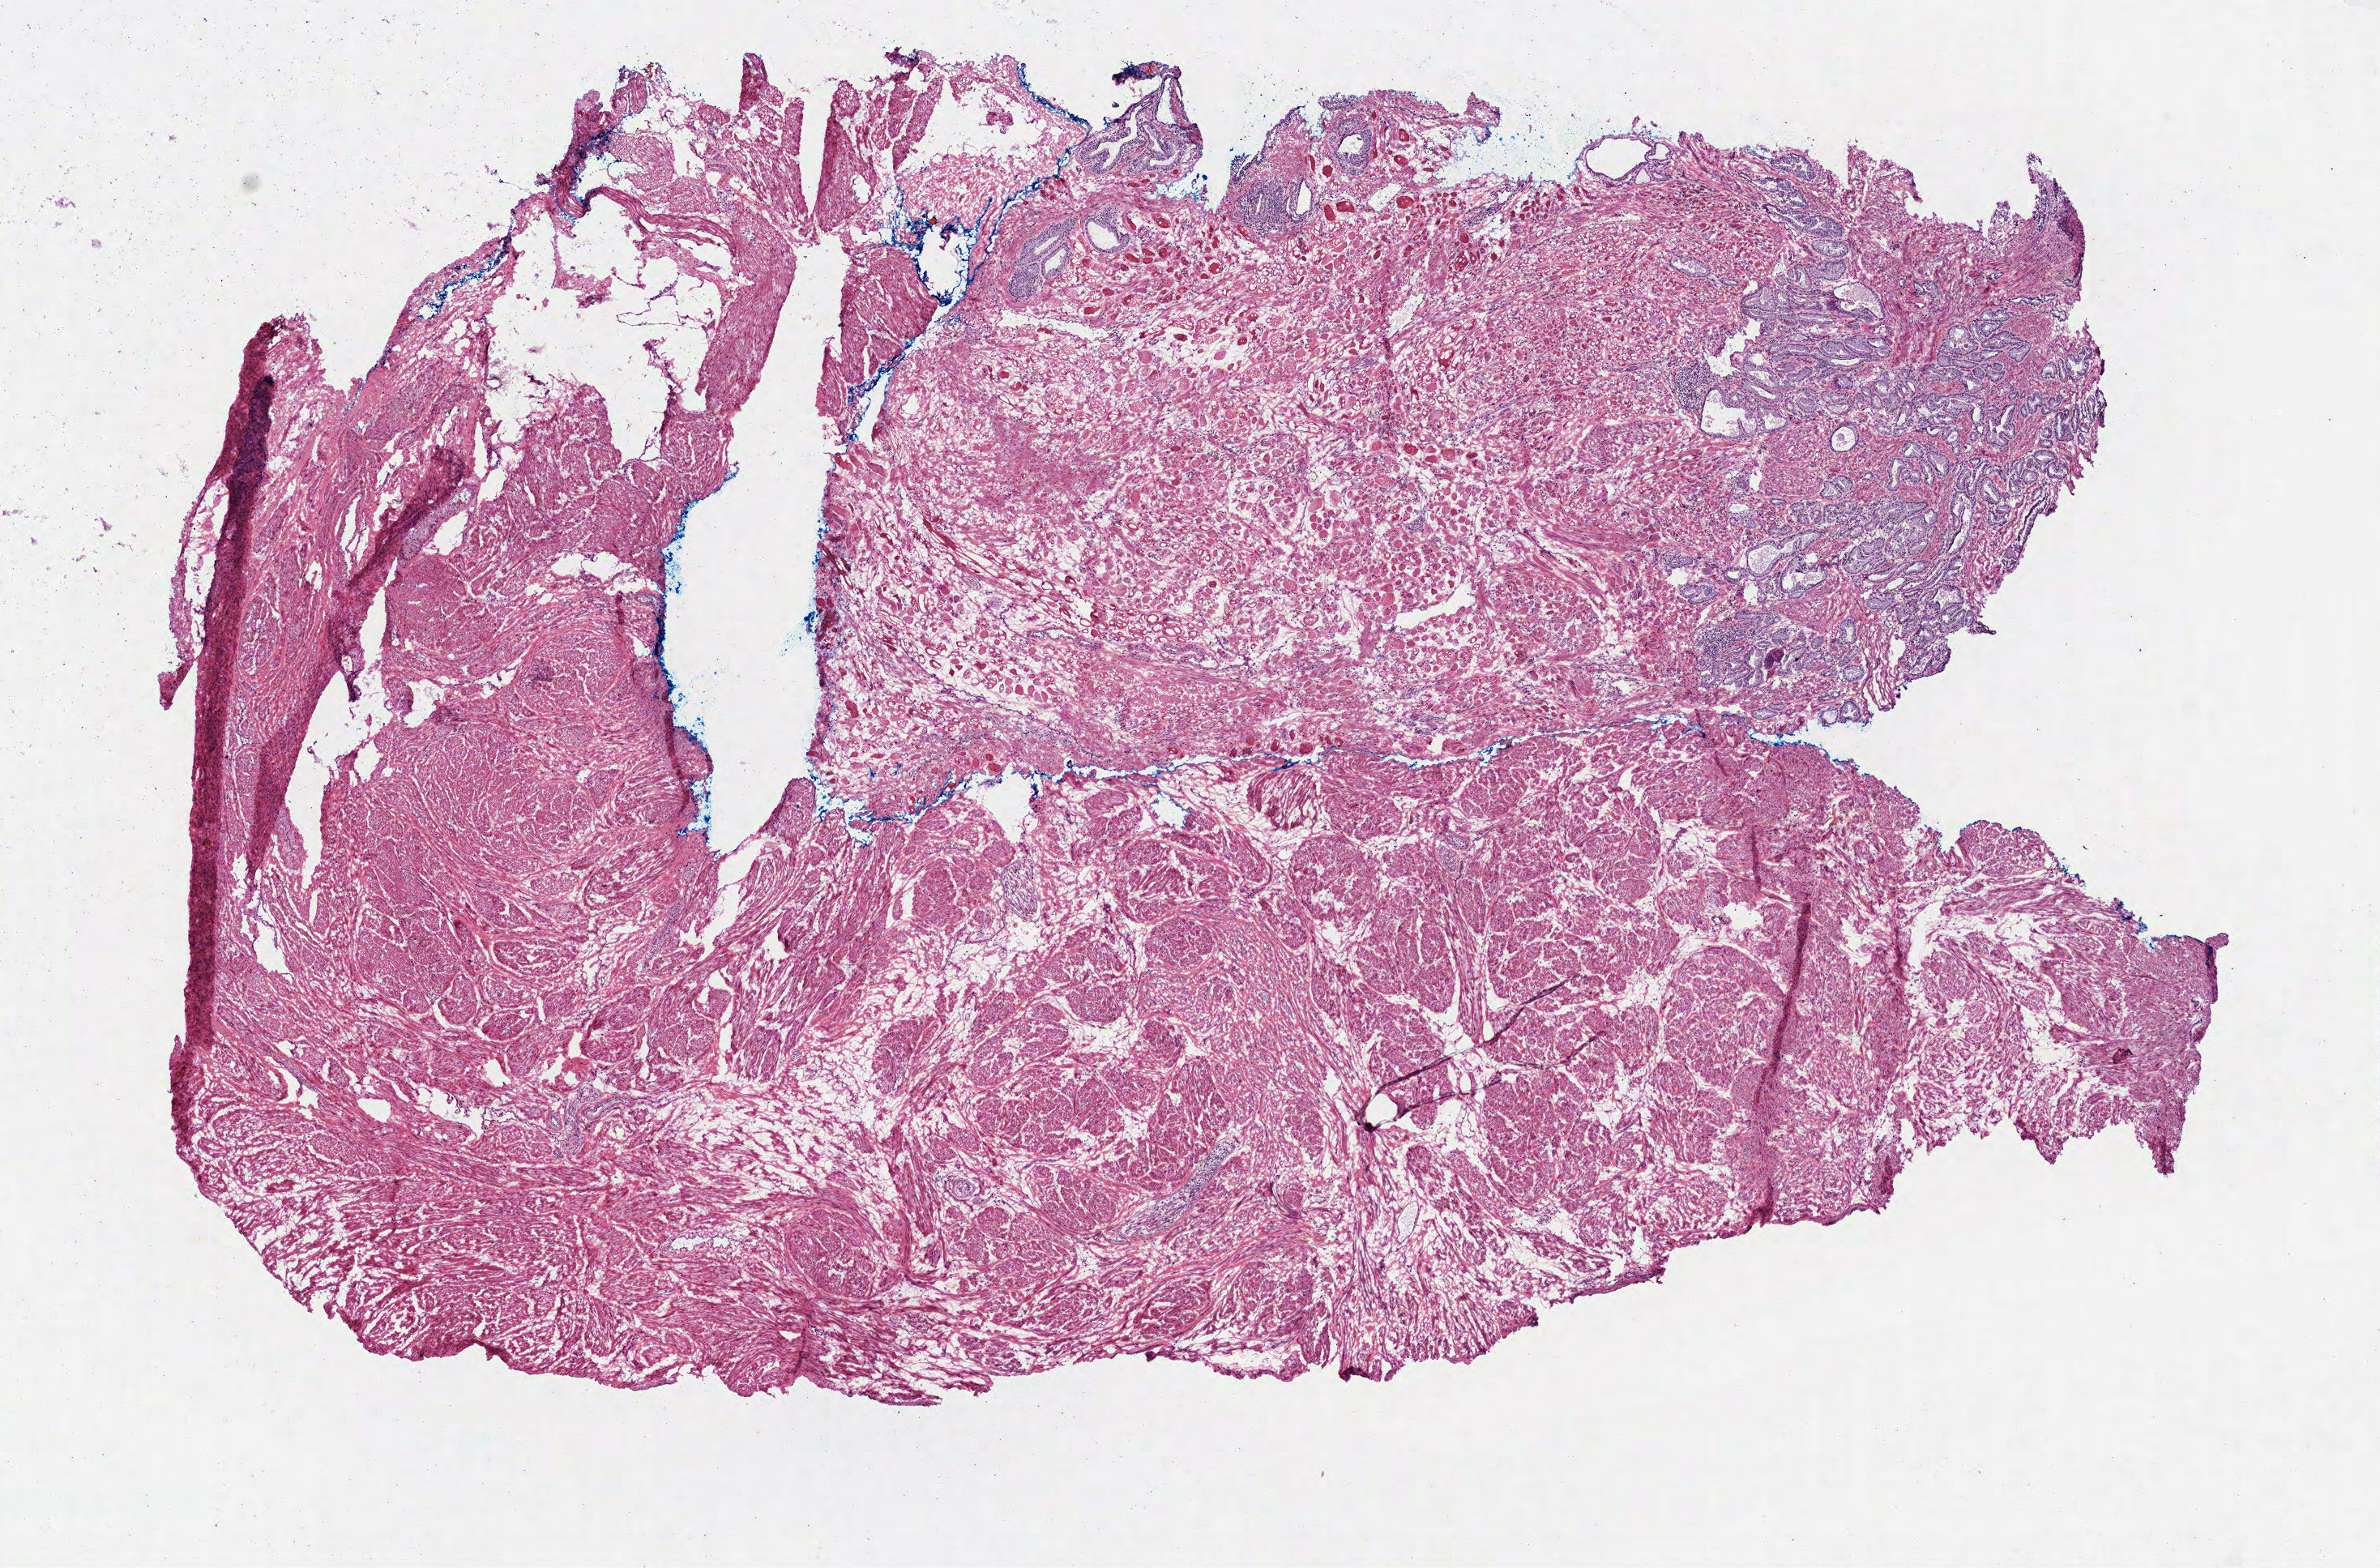
Hematoxylin and eosin (H&E) stained whole-slide image, low-resolution overview of the scanned area, about 11.8 x 7.8 mm (slide scanned at 40x). Frozen section. Solid tissue normal (non-tumour tissue) sample from the prostate. Male patient; age at initial diagnosis 50 years.
This section: solid tissue normal (non-tumour) sample from the same patient. Patient diagnosis: Acinar cell carcinoma (prostate gland).